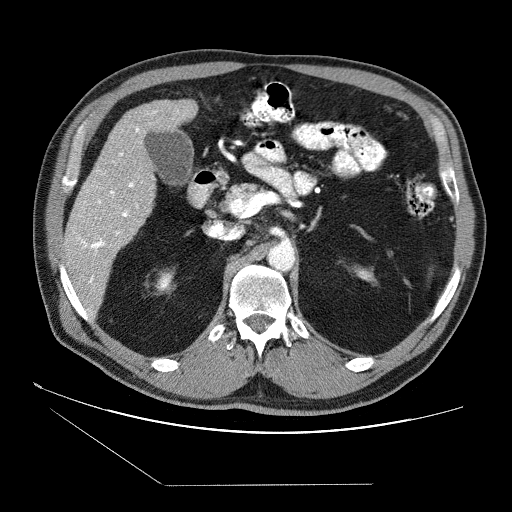
Contrast-enhanced abdominal CT (liver protocol), one axial slice. Reconstruction kernel STANDARD. Soft-tissue window (W 400 / L 40 HU). 512 × 512 image matrix, field of view 400 × 400 mm. From the clinical record (not read from this slice): diagnosis: hepatocellular carcinoma (patient treated with transarterial chemoembolisation; whether this scan precedes or follows treatment is not stated here); TNM stage (as recorded): Stage-II; Child-Pugh class: B; tumour differentiation: no biopsy; tumour nodularity: multinodular.
Annotated regions visible in this slice (semi-automatically segmented with operator editing):
- liver parenchyma outside the tumour (the mass and vessels are separate outlines, so this box may not span the whole liver): bounding box <62,100,198,294> (left, top, right, bottom; pixels)
- liver vessels: <77,111,157,283>